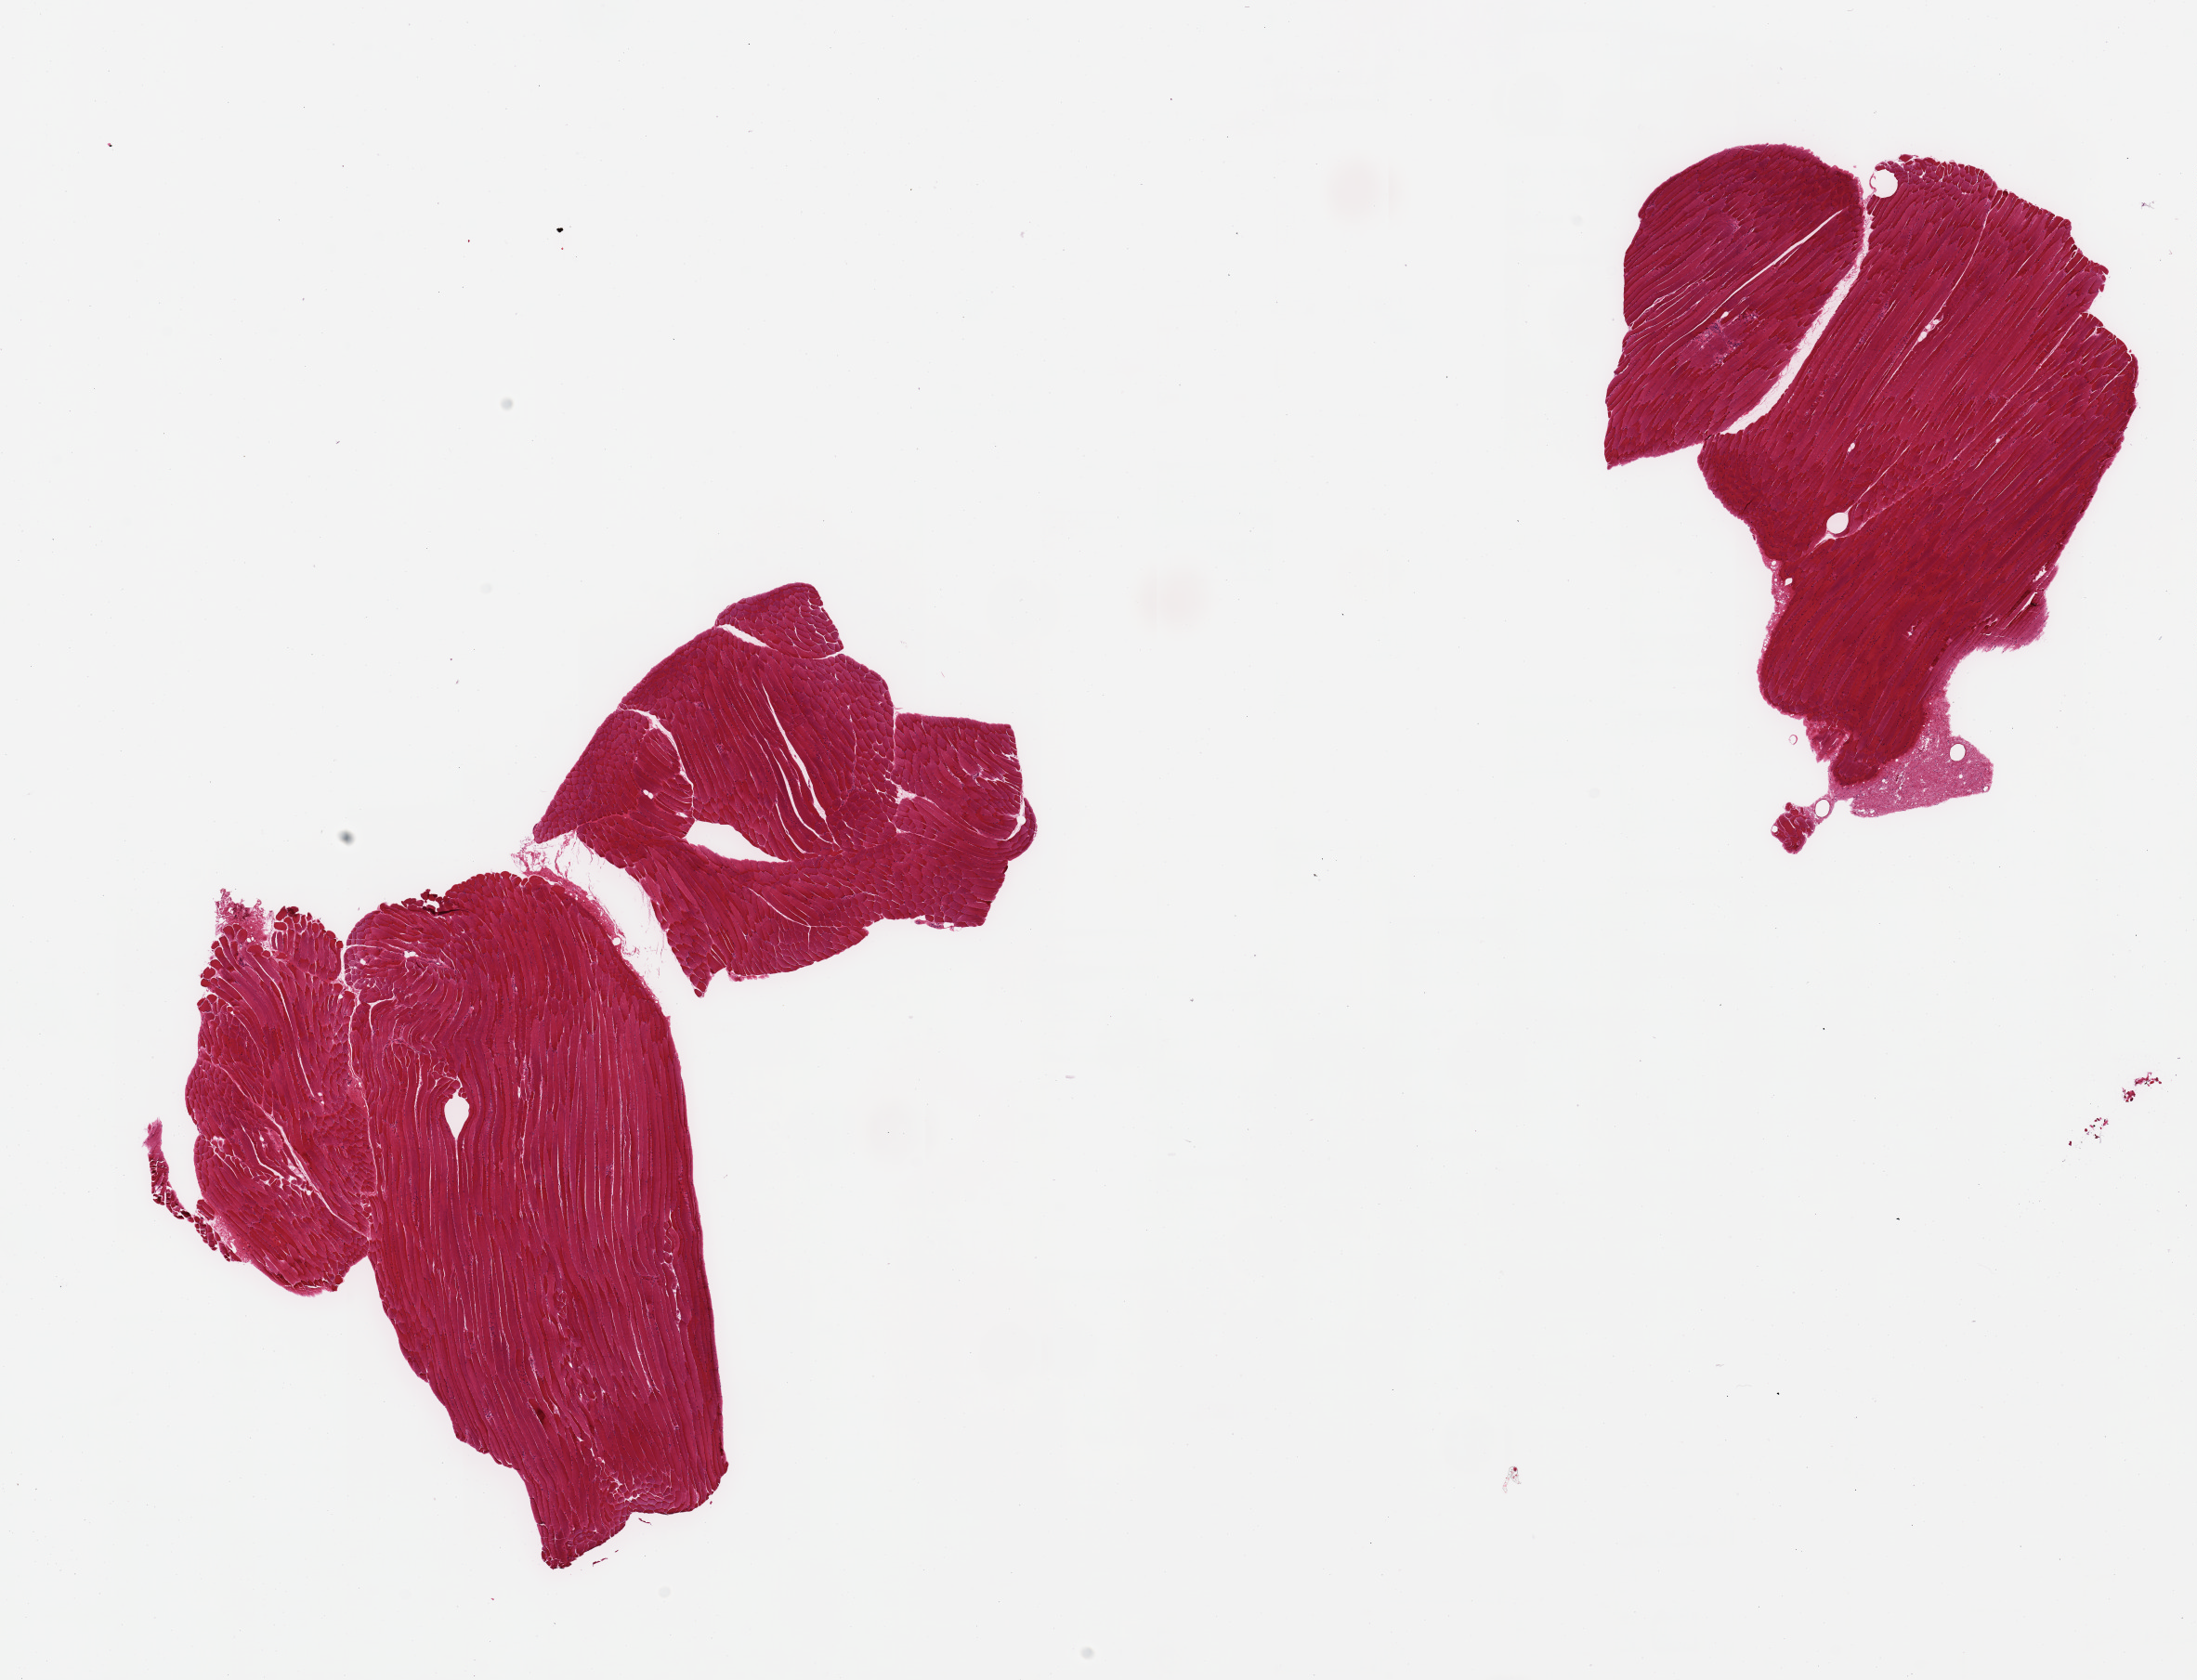
Digitized H&E-stained section, brightfield — a low-resolution overview of the entire scanned area, about 18.7 x 14.3 mm (slide scanned at 20x), PAXgene-fixed paraffin-embedded (PFPE) section, sampled site (target tissue): skeletal muscle, donor tissue sample.
Reviewer comment on this tissue sample: 2 pieces, trace interstitial fat.